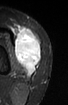
MRI of an extremity soft-tissue mass, one axial slice. Slice 28 of 52 in the series (ordered by position). STIR. MR volume resampled by the dataset authors to the PET/CT grid (not the native acquisition matrix). 3.27 mm slice thickness. 68 × 105 image matrix. Female patient. Case-level facts recorded for this patient, not image findings: histological type: spindle cell suggestive of biphasic synovial sarcoma; grade: intermediate; site of the primary tumour: left knee.
Structures marked on this image (expert contour drawn on MRI and transferred to this co-registered scan by the dataset authors):
- gross tumour volume including surrounding oedema: bounding box (x1, y1, x2, y2) in pixels: (12, 27, 41, 76)
- gross tumour volume (mass): (14, 29, 41, 76)